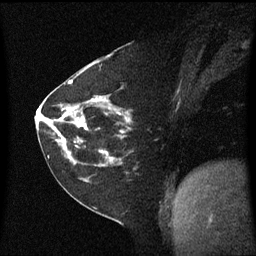
Breast MRI (dynamic contrast-enhanced), one sagittal slice. Dynamic contrast-enhanced series, image 2 of 3 at this slice position (ordered by acquisition). 1.5 T. TE 4.2 ms, TR 8.4 ms. 2 mm slice thickness. 256 × 256 image matrix, field of view 210 × 210 mm. Patient: female, 60 years. From the clinical record (not read from this slice): setting: breast cancer imaged before/during neoadjuvant chemotherapy; receptor status: triple-negative.
Structures marked on this image (semi-automatically segmented with operator editing):
- analysis volume of interest (the breast-tissue region the enhancement analysis was run in; not a lesion): box from (x=45, y=99) to (x=134, y=182) px
- tumour enhancement mask (voxels above the 70 % enhancement threshold inside the analysis volume of interest): (x=54, y=99)–(x=130, y=162)